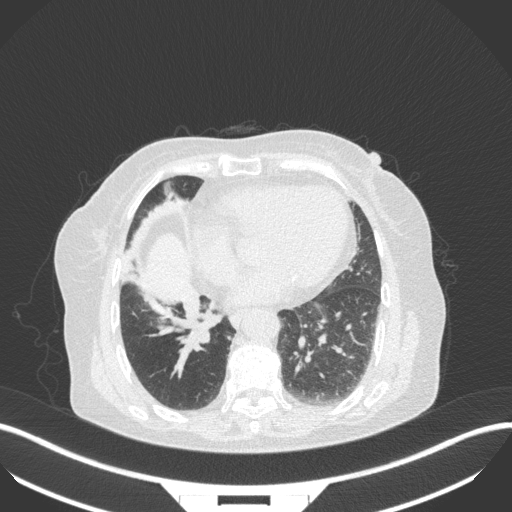
Chest CT, one axial slice; slice 114 of 329 in the series (ordered by position); 120 kVp; lung window (W 1500 / L -600 HU); 1 mm slice thickness; 512 × 512 image matrix. Patient: female, 75 years. Case-level facts recorded for this patient, not image findings: clinical TNM (as recorded): T1b N0 M1a; histopathological grade: G1.
Outlined on this slice (bounding box drawn by a radiologist):
- lung tumour (recorded histology: squamous cell carcinoma): bounding box [x1, y1, x2, y2] px = [181, 301, 219, 354]